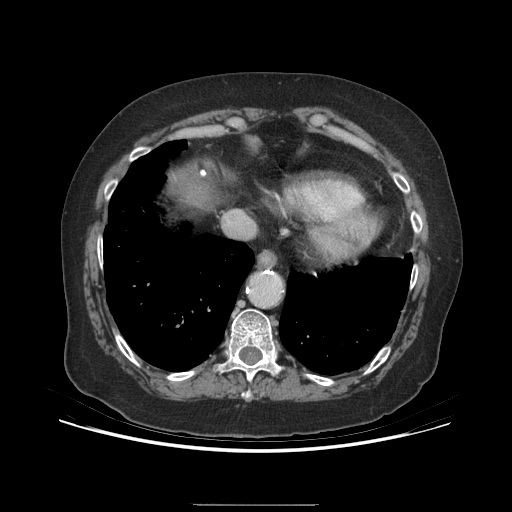
Contrast-enhanced abdominal CT (liver protocol), one axial slice. Slice 181 of 192 in the series (ordered by position). Reconstruction kernel STANDARD. Soft-tissue window (W 400 / L 40 HU). 512 × 512 image matrix, field of view 400 × 400 mm. From the clinical record (not read from this slice): diagnosis: hepatocellular carcinoma (patient treated with transarterial chemoembolisation; whether this scan precedes or follows treatment is not stated here); TNM stage (as recorded): Stage-I; Child-Pugh class: A; tumour differentiation: moderately differentiated; tumour size: 3.2 cm.
Outlined on this slice (semi-automatically segmented with operator editing):
- abdominal aorta: box from (x=251, y=273) to (x=280, y=305) px
- liver parenchyma outside the tumour (the mass and vessels are separate outlines, so this box may not span the whole liver): (x=168, y=166)–(x=210, y=206)
- liver vessels: (x=201, y=171)–(x=205, y=175)